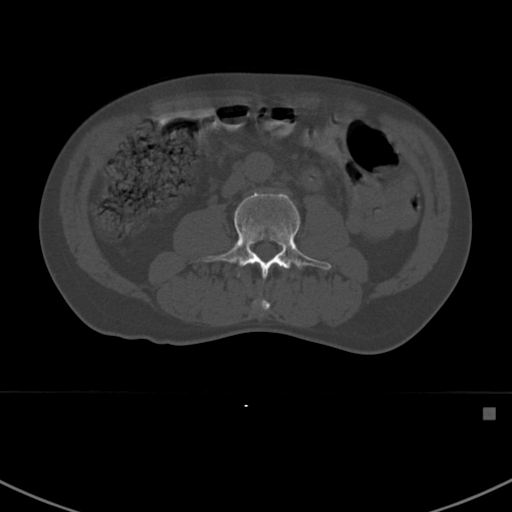
CT including the spine, one axial slice. Position 265 of 412 along the scan axis. 120 kVp. Bone window (W 1800 / L 400 HU). 1.5 mm slice thickness. 512 × 512 image matrix, field of view 358 × 358 mm. Patient: male, 59 years. From the clinical record (not read from this slice): primary cancer: prostate.
Structures marked on this image (semi-automatic segmentation, software-assisted and operator-edited):
- L2 vertebra: bounding box <253,299,270,311> (left, top, right, bottom; pixels)
- L3 vertebra: <196,191,331,279>